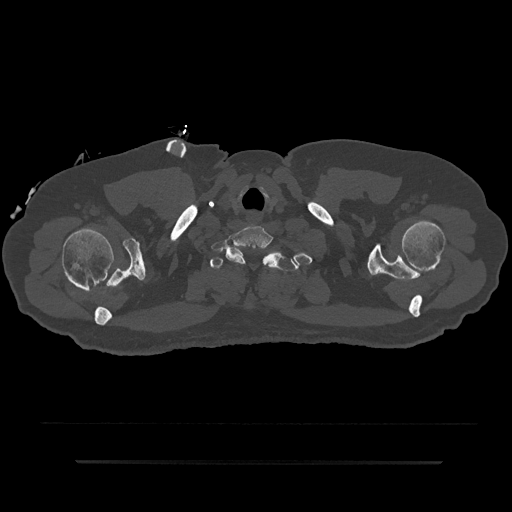
CT including the spine, one axial slice. Position 757 of 797 along the scan axis. Reconstruction kernel Br40s/3. Bone window (W 1800 / L 400 HU). 0.5 mm slice thickness. 512 × 512 image matrix. Patient: male, 59 years. Case-level facts recorded for this patient, not image findings: primary cancer: bile ducts; vertebrae with lytic lesions (as recorded): T10.
Annotated regions visible in this slice (semi-automatically segmented with operator editing):
- T1 vertebra: box from (x=210, y=252) to (x=299, y=271) px